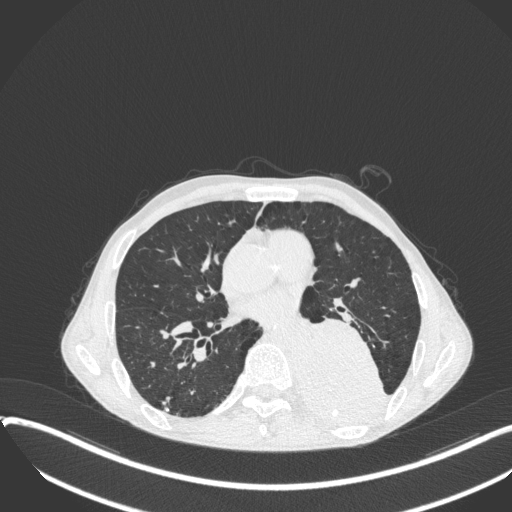
Chest CT, one axial slice. Position 181 of 400 along the scan axis. Reconstruction kernel B31f. 120 kVp. Lung window (W 1500 / L -600 HU). 1 mm slice thickness. 512 × 512 image matrix. Patient: male, 57 years. From the clinical record (not read from this slice): clinical TNM (as recorded): T4 N0 M0.
Annotated regions visible in this slice (bounding box drawn by a radiologist):
- lung tumour (recorded histology: squamous cell carcinoma): bounding box <301,316,389,421> (left, top, right, bottom; pixels)